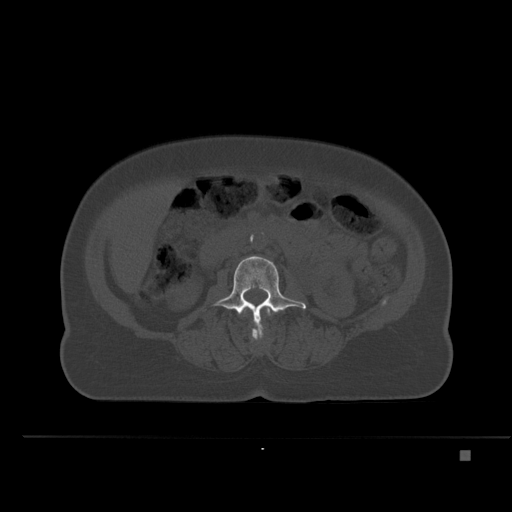
CT including the spine, one axial slice; position 200 of 477 along the scan axis; bone window (W 1800 / L 400 HU); 512 × 512 image matrix, field of view 422 × 422 mm. Patient: female, 74 years. Case-level facts recorded for this patient, not image findings: primary cancer: colon.
Outlined on this slice (semi-automatic segmentation, software-assisted and operator-edited):
- L2 vertebra: bounding box [x1, y1, x2, y2] px = [244, 308, 271, 342]
- L3 vertebra: [213, 256, 306, 335]